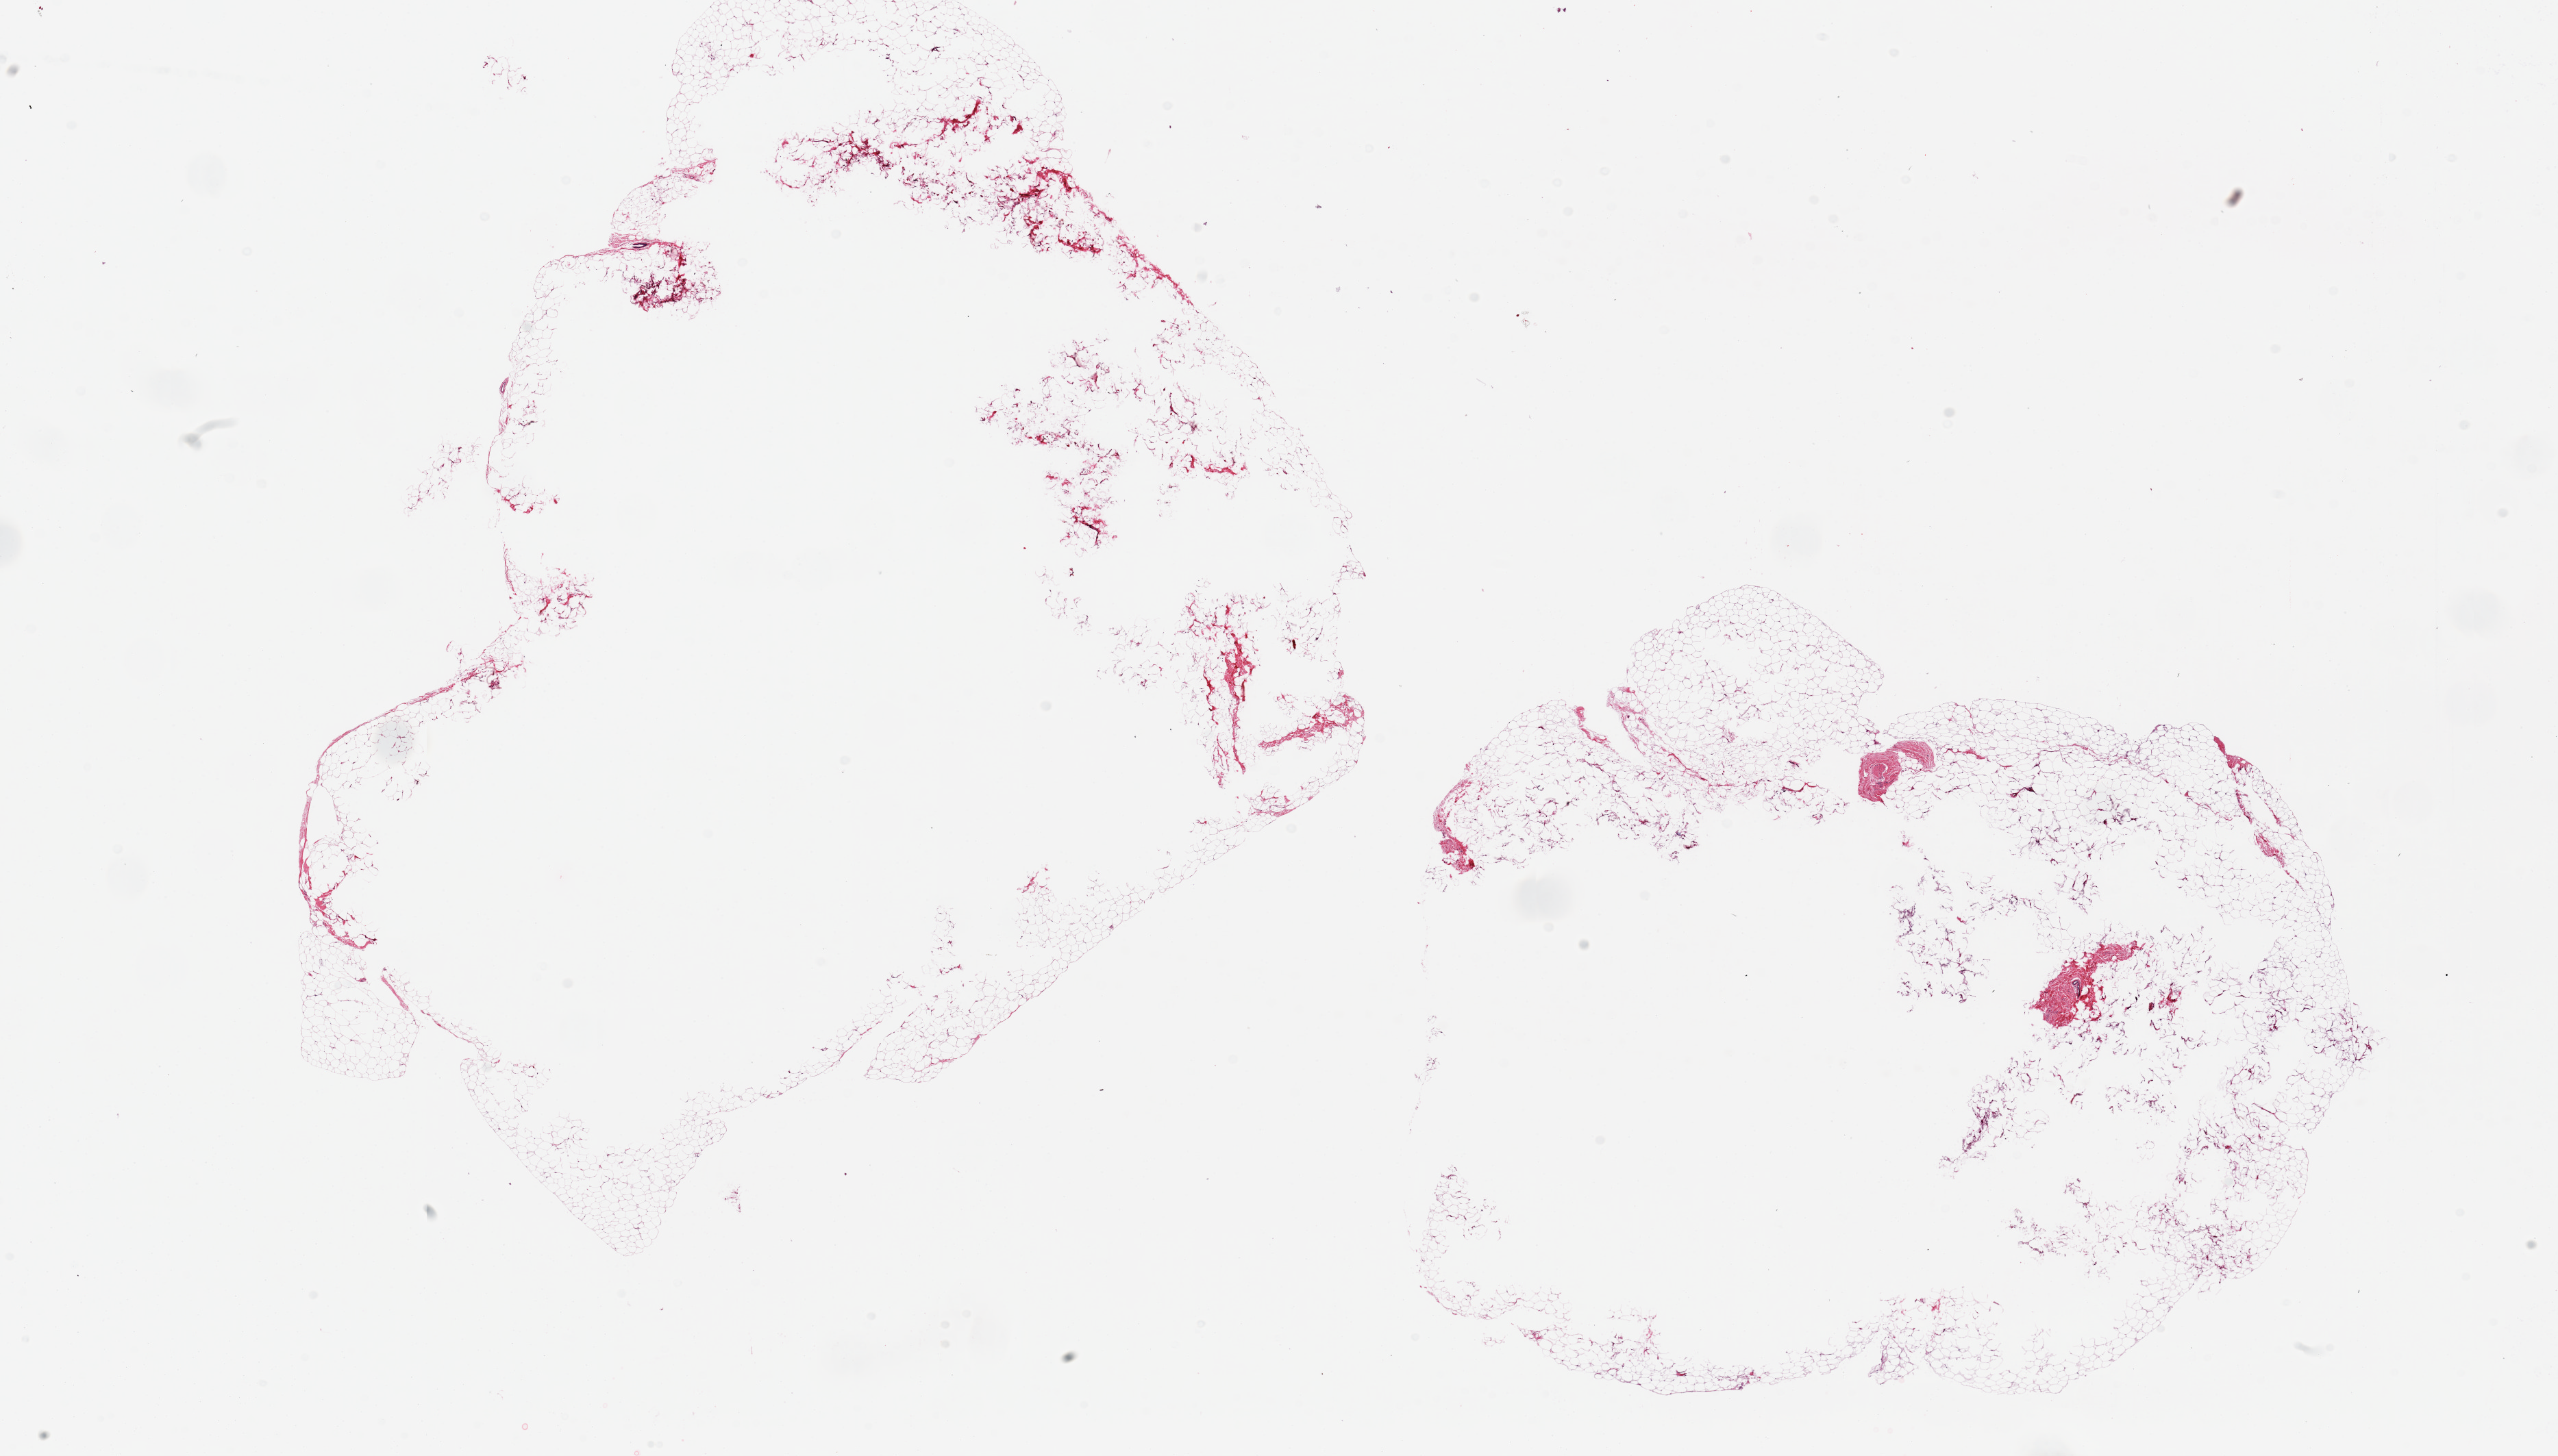
Whole-slide image, H&E stain — whole scanned area (about 29.5 x 16.8 mm) shown as a low-resolution overview. PAXgene-fixed paraffin-embedded (PFPE) section. Target tissue: breast. Donor tissue sample.
Reviewer comment on this tissue sample: 2 pieces 12x8mm.